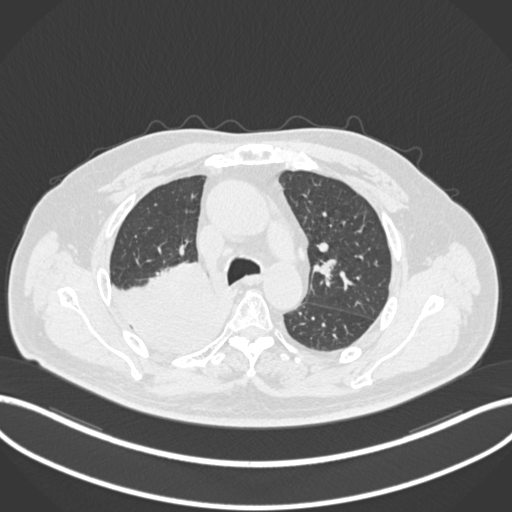
Chest CT, one axial slice. Slice 138 of 218 in the series (ordered by position). Reconstruction kernel B30f. 120 kVp. Lung window (W 1500 / L -600 HU). 512 × 512 image matrix, field of view 400 × 400 mm. Patient: male, 68 years. From the clinical record (not read from this slice): clinical TNM (as recorded): T2a N0 M0.
Annotated regions visible in this slice (rectangle marked by the reading radiologist):
- lung tumour (recorded histology: adenocarcinoma): bounding box <111,263,239,357> (left, top, right, bottom; pixels)